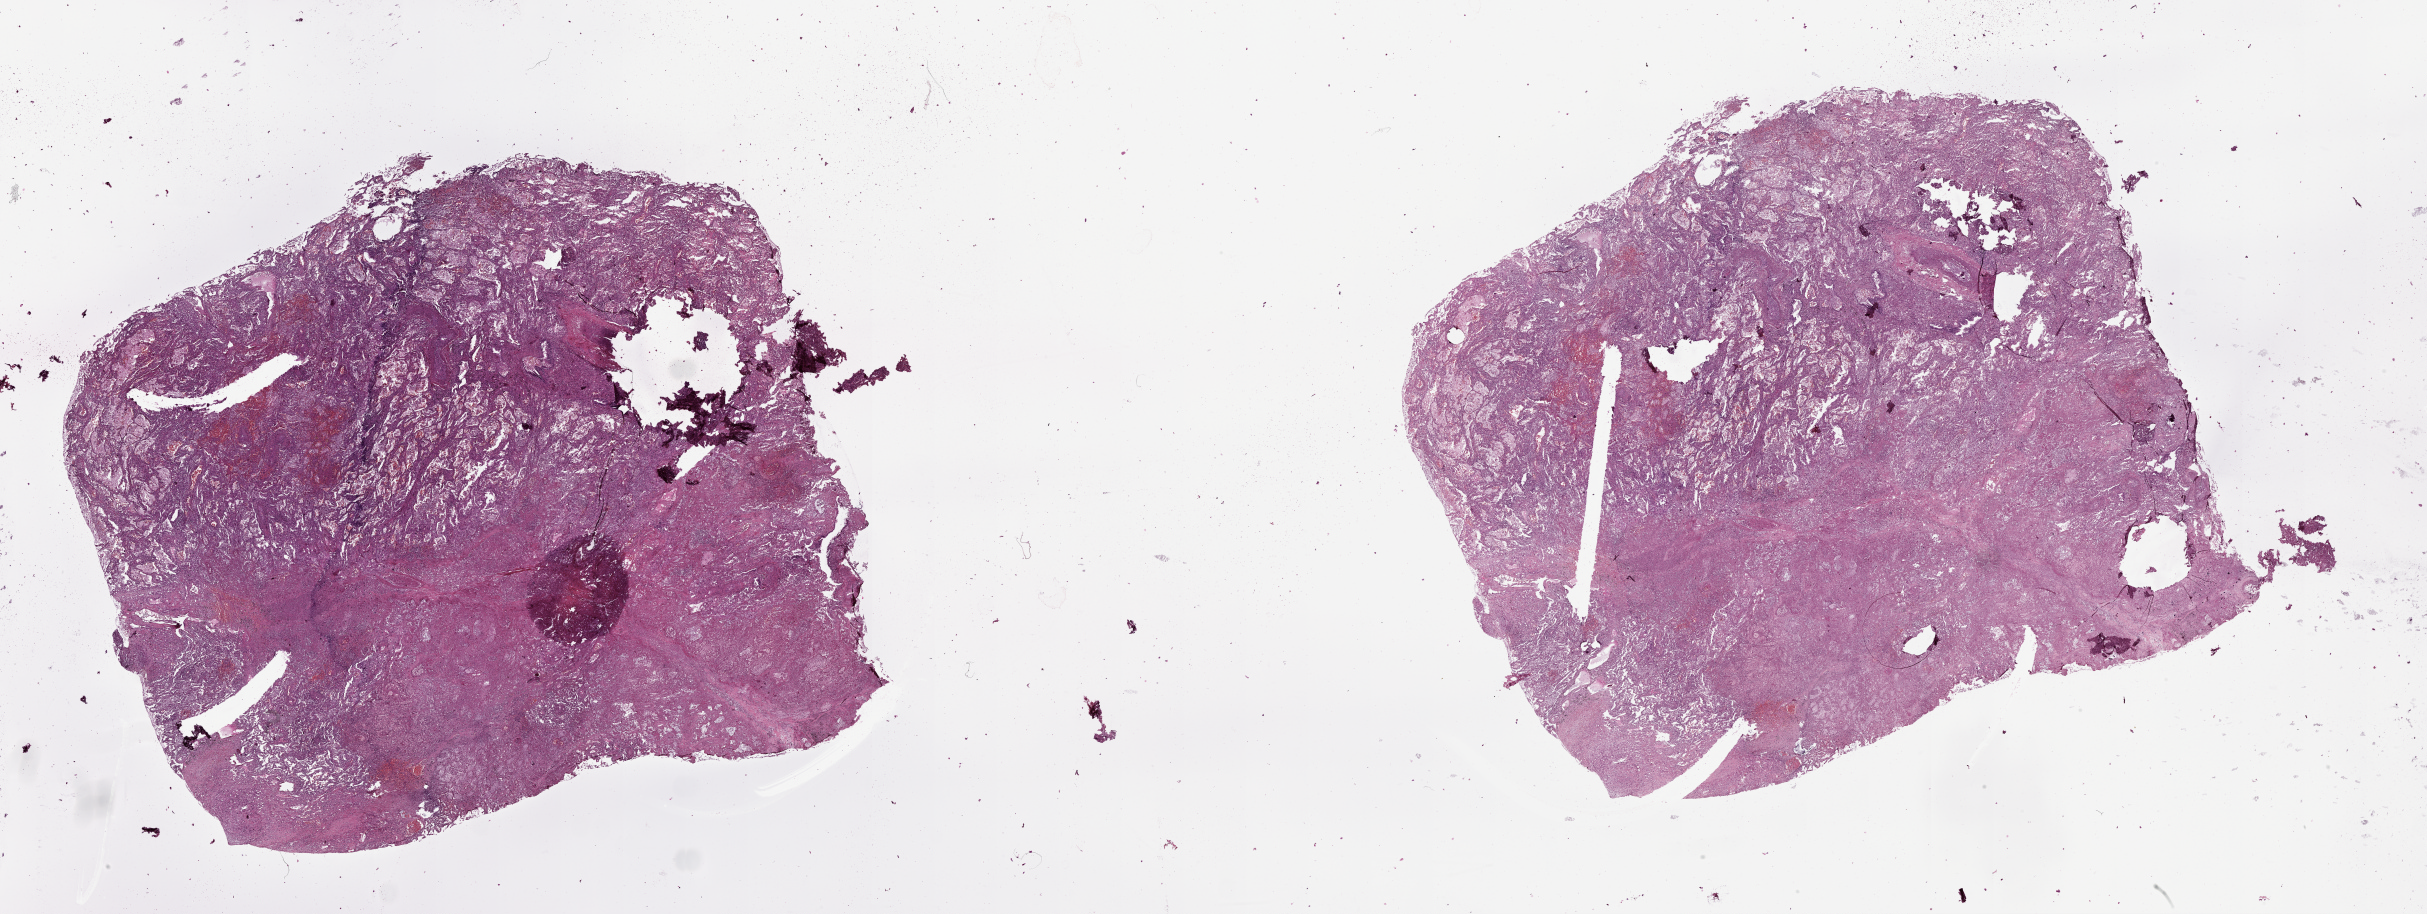
Hematoxylin and eosin (H&E) stained whole-slide image, shown as a low-resolution overview of the whole scanned area (about 39.1 x 14.7 mm, acquisition: 20x scan); lung, normal (non-tumour) tissue. Patient: male, age 68 years.
- this section: normal (non-tumour) tissue from the same patient
- patient diagnosis (cohort enrolment): squamous cell carcinoma (lung)